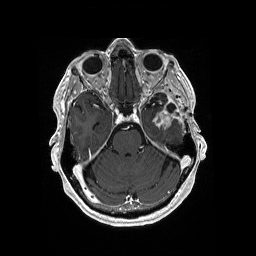
Brain MRI from a brain-tumour surgery series, one axial slice; slice 122 of 176 in the series (ordered by position); T1-weighted post-contrast; 1 mm slice thickness; 256 × 256 image matrix, field of view 256 × 256 mm. Case-level facts recorded for this patient, not image findings: histopathology: Glioblastoma; WHO grade: 4; IDH mutation: no; tumour location: Left Medial Temporal.
Outlined on this slice (outlined manually by an expert reader):
- previous resection cavity: bounding box (x1, y1, x2, y2) in pixels: (166, 104, 176, 112)
- tumour: (152, 112, 175, 129)